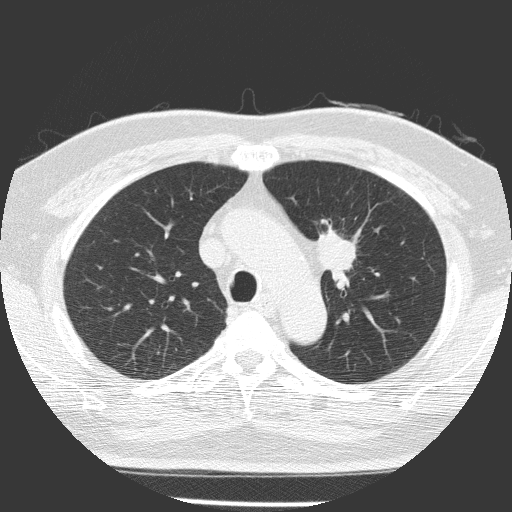
Low-dose screening chest CT, axial slice, first (baseline) screen, lung window (W 1500 / L -600 HU), 120 kVp, slice 46 of 156 in the series. Male participant, aged 70 years at enrolment. Current smoker at enrolment.
Expert reader's lesion annotation, bounding box (x1, y1, x2, y2) in pixels: (298, 223, 371, 297). The screening reader recorded 3 non-calcified nodules or masses ≥4 mm on this exam; which of them this box marks is not recorded. Official screen result: positive, change unspecified: nodule(s) >= 4 mm or enlarging nodule(s), mass(es), or other non-specific abnormalities suspicious for lung cancer. Lung cancer was diagnosed 58 days after this screen: squamous cell carcinoma, NOS, left upper lobe, poorly differentiated (G3), stage IB (AJCC 6th edition), 47 mm at pathology.